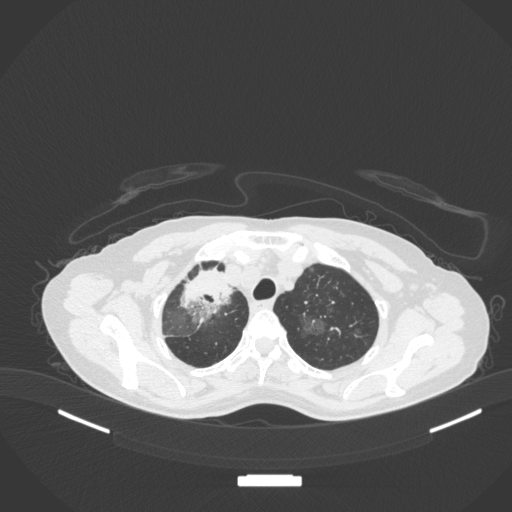
Chest CT, one axial slice. Slice 272 of 311 in the series (ordered by position). Reconstruction kernel B31f. Lung window (W 1500 / L -600 HU). 1 mm slice thickness. 512 × 512 image matrix, field of view 400 × 400 mm. Female patient, age 59 years. From the clinical record (not read from this slice): clinical TNM (as recorded): T3 N0 M0.
Outlined on this slice (bounding box drawn by a radiologist):
- lung tumour (recorded histology: adenocarcinoma): bounding box [x1, y1, x2, y2] px = [172, 258, 234, 325]